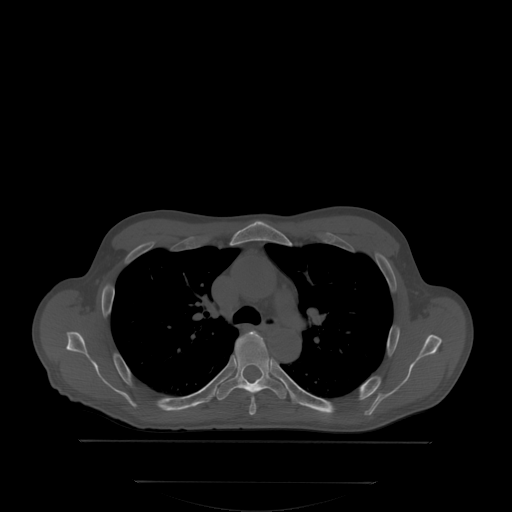
CT including the spine, one axial slice. Slice 250 of 350 in the series (ordered by position). Bone window (W 1800 / L 400 HU). 2.5 mm slice thickness. 512 × 512 image matrix. Patient: male, 58 years. Case-level facts recorded for this patient, not image findings: primary cancer: prostate; vertebrae with lytic lesions (as recorded): L1.
Outlined on this slice (semi-automatic segmentation, software-assisted and operator-edited):
- T4 vertebra: bounding box [x1, y1, x2, y2] px = [250, 393, 256, 415]
- T5 vertebra: [215, 330, 287, 401]